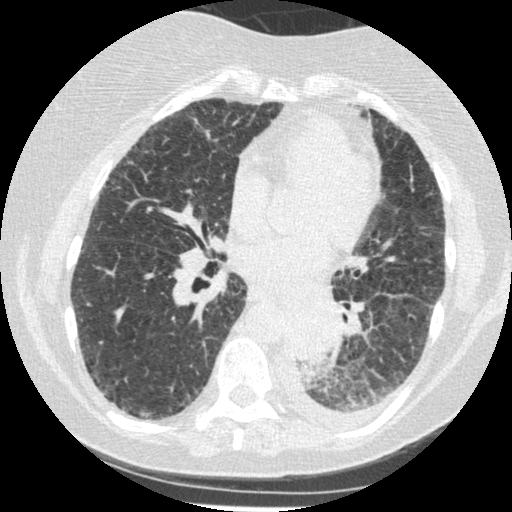
Low-dose screening chest CT, one axial slice. Slice 106 of 341 in the series (ordered by position). Lung window (W 1500 / L -600 HU). 512 × 512 image matrix, field of view 310 × 310 mm.
Structures marked on this image (expert manual segmentation):
- lesion 1 (tumor, lower lobe of left lung): bounding box (x1, y1, x2, y2) in pixels: (285, 303, 339, 364)